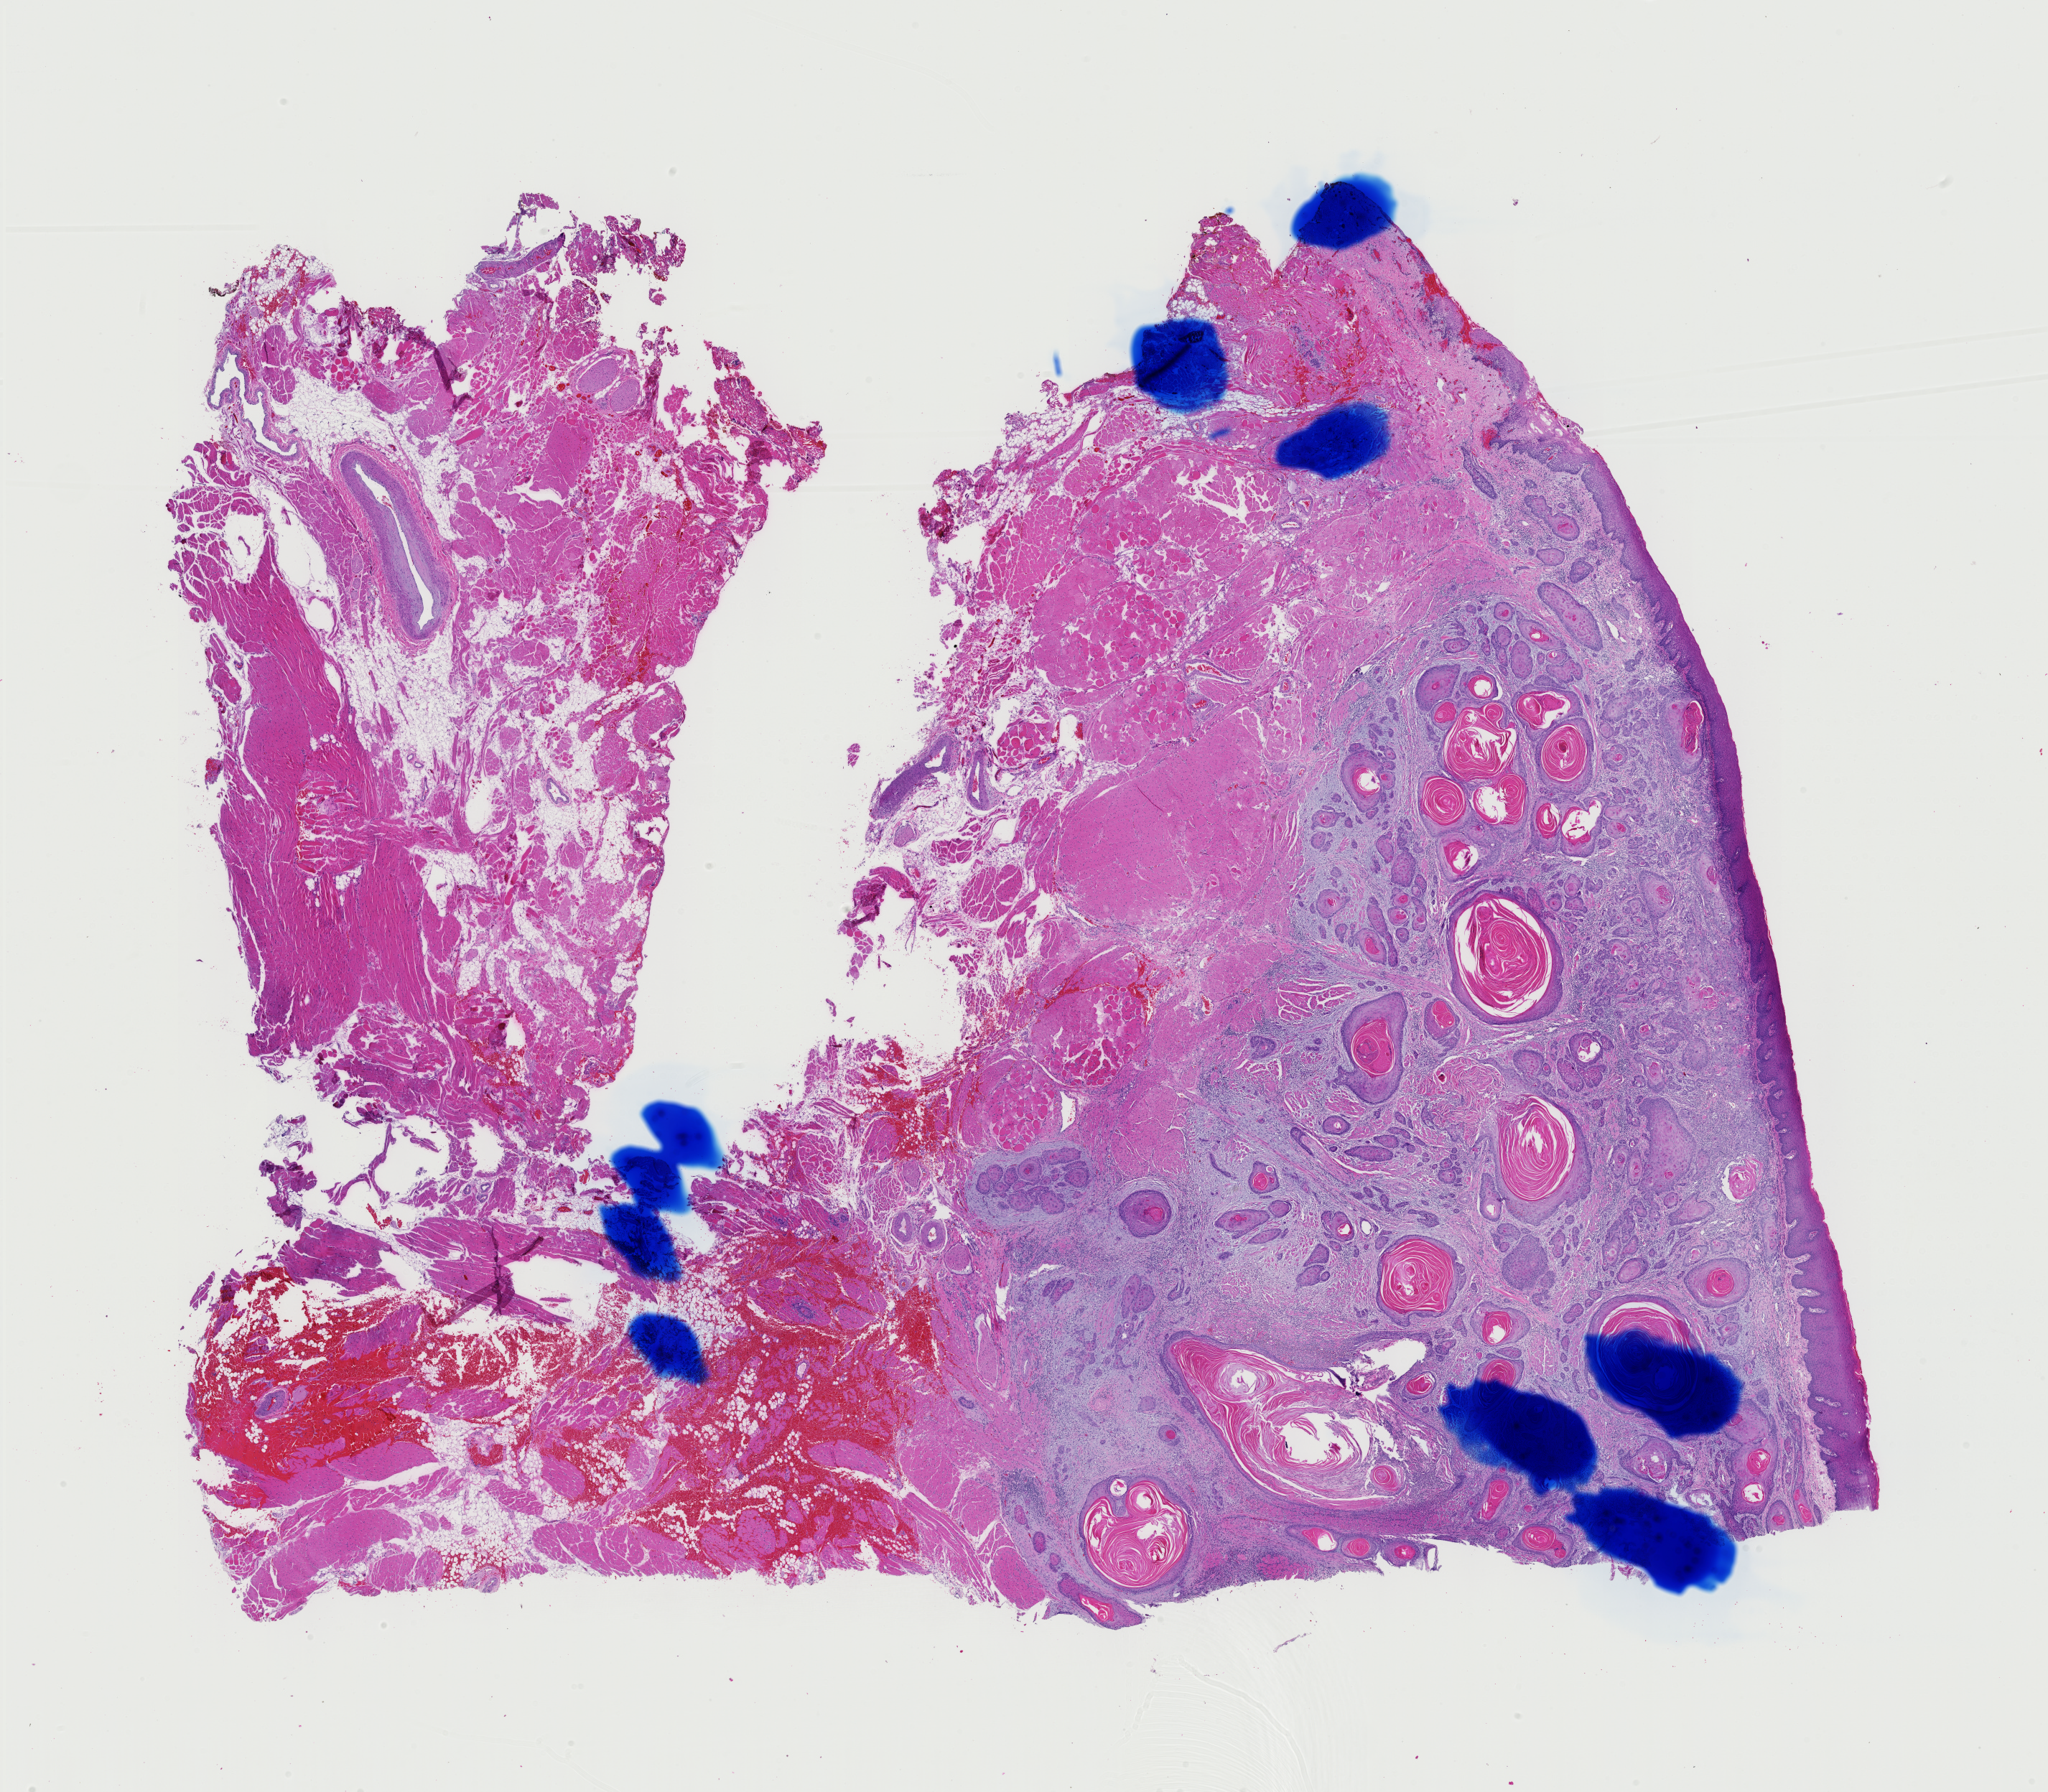
H&E-stained whole-slide image, whole scanned area (about 20.7 x 18.1 mm) shown as a low-resolution overview. Formalin-fixed paraffin-embedded (FFPE) diagnostic section. Sample: primary tumour, head and neck. Male patient; age at initial diagnosis 60 years. Histologic grade: G2 (moderately differentiated).
AJCC pathologic stage: III. Lymph nodes positive (case pathology): 1 of 39 examined. Diagnosis: Squamous cell carcinoma, NOS (tongue, NOS).